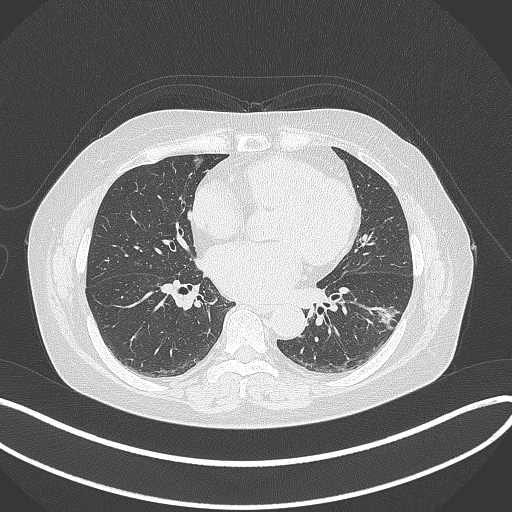
Chest CT, one axial slice; position 158 of 373 along the scan axis; reconstruction kernel B70f; lung window (W 1500 / L -600 HU); 512 × 512 image matrix, field of view 400 × 400 mm. Female patient, age 67 years. From the clinical record (not read from this slice): clinical TNM (as recorded): T1c N0 M0; histopathological grade: G2.
Structures marked on this image (bounding box drawn by a radiologist):
- lung tumour (recorded histology: adenocarcinoma): box from (x=364, y=300) to (x=401, y=332) px